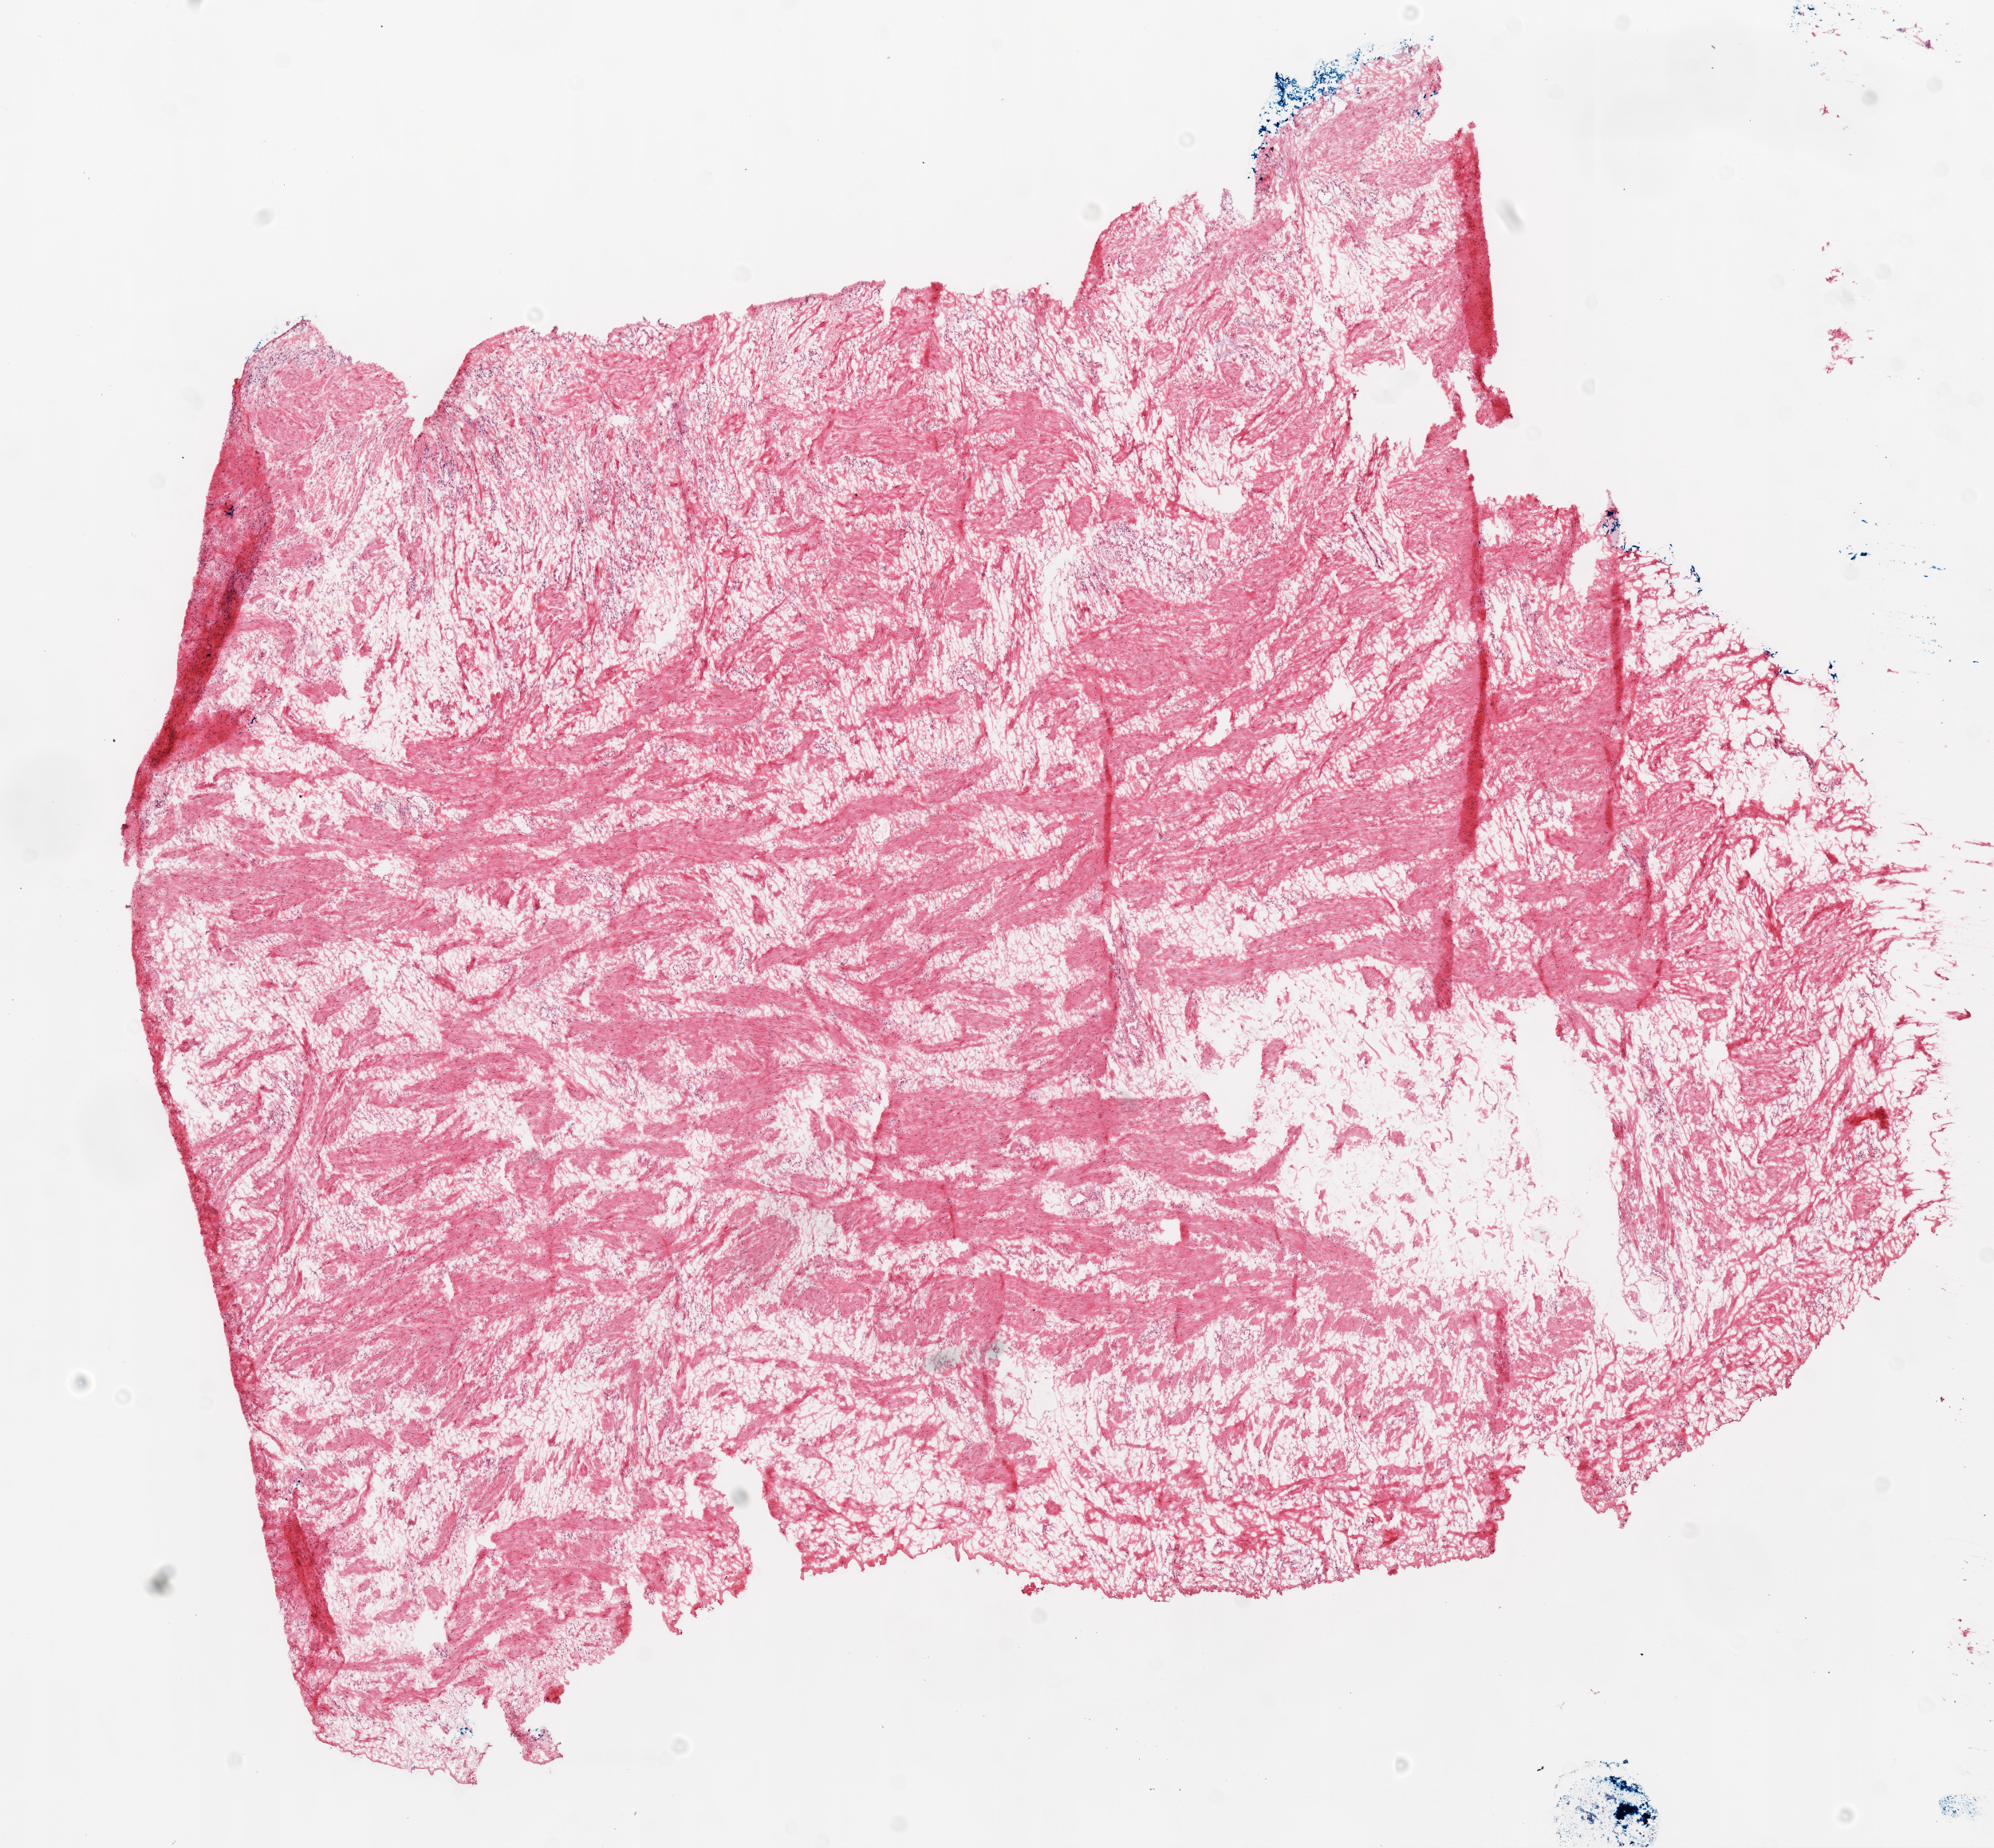
Whole-slide histology image, H&E-stained, low-resolution overview of the scanned area, about 10.0 x 9.3 mm (acquisition: 20x scan), frozen section from the top of the tissue portion, sample: solid tissue normal (non-tumour tissue), ovary. Patient: female, age at initial diagnosis 56 years.
* this section: solid tissue normal (non-tumour) sample from the same patient
* patient diagnosis: Serous cystadenocarcinoma, NOS